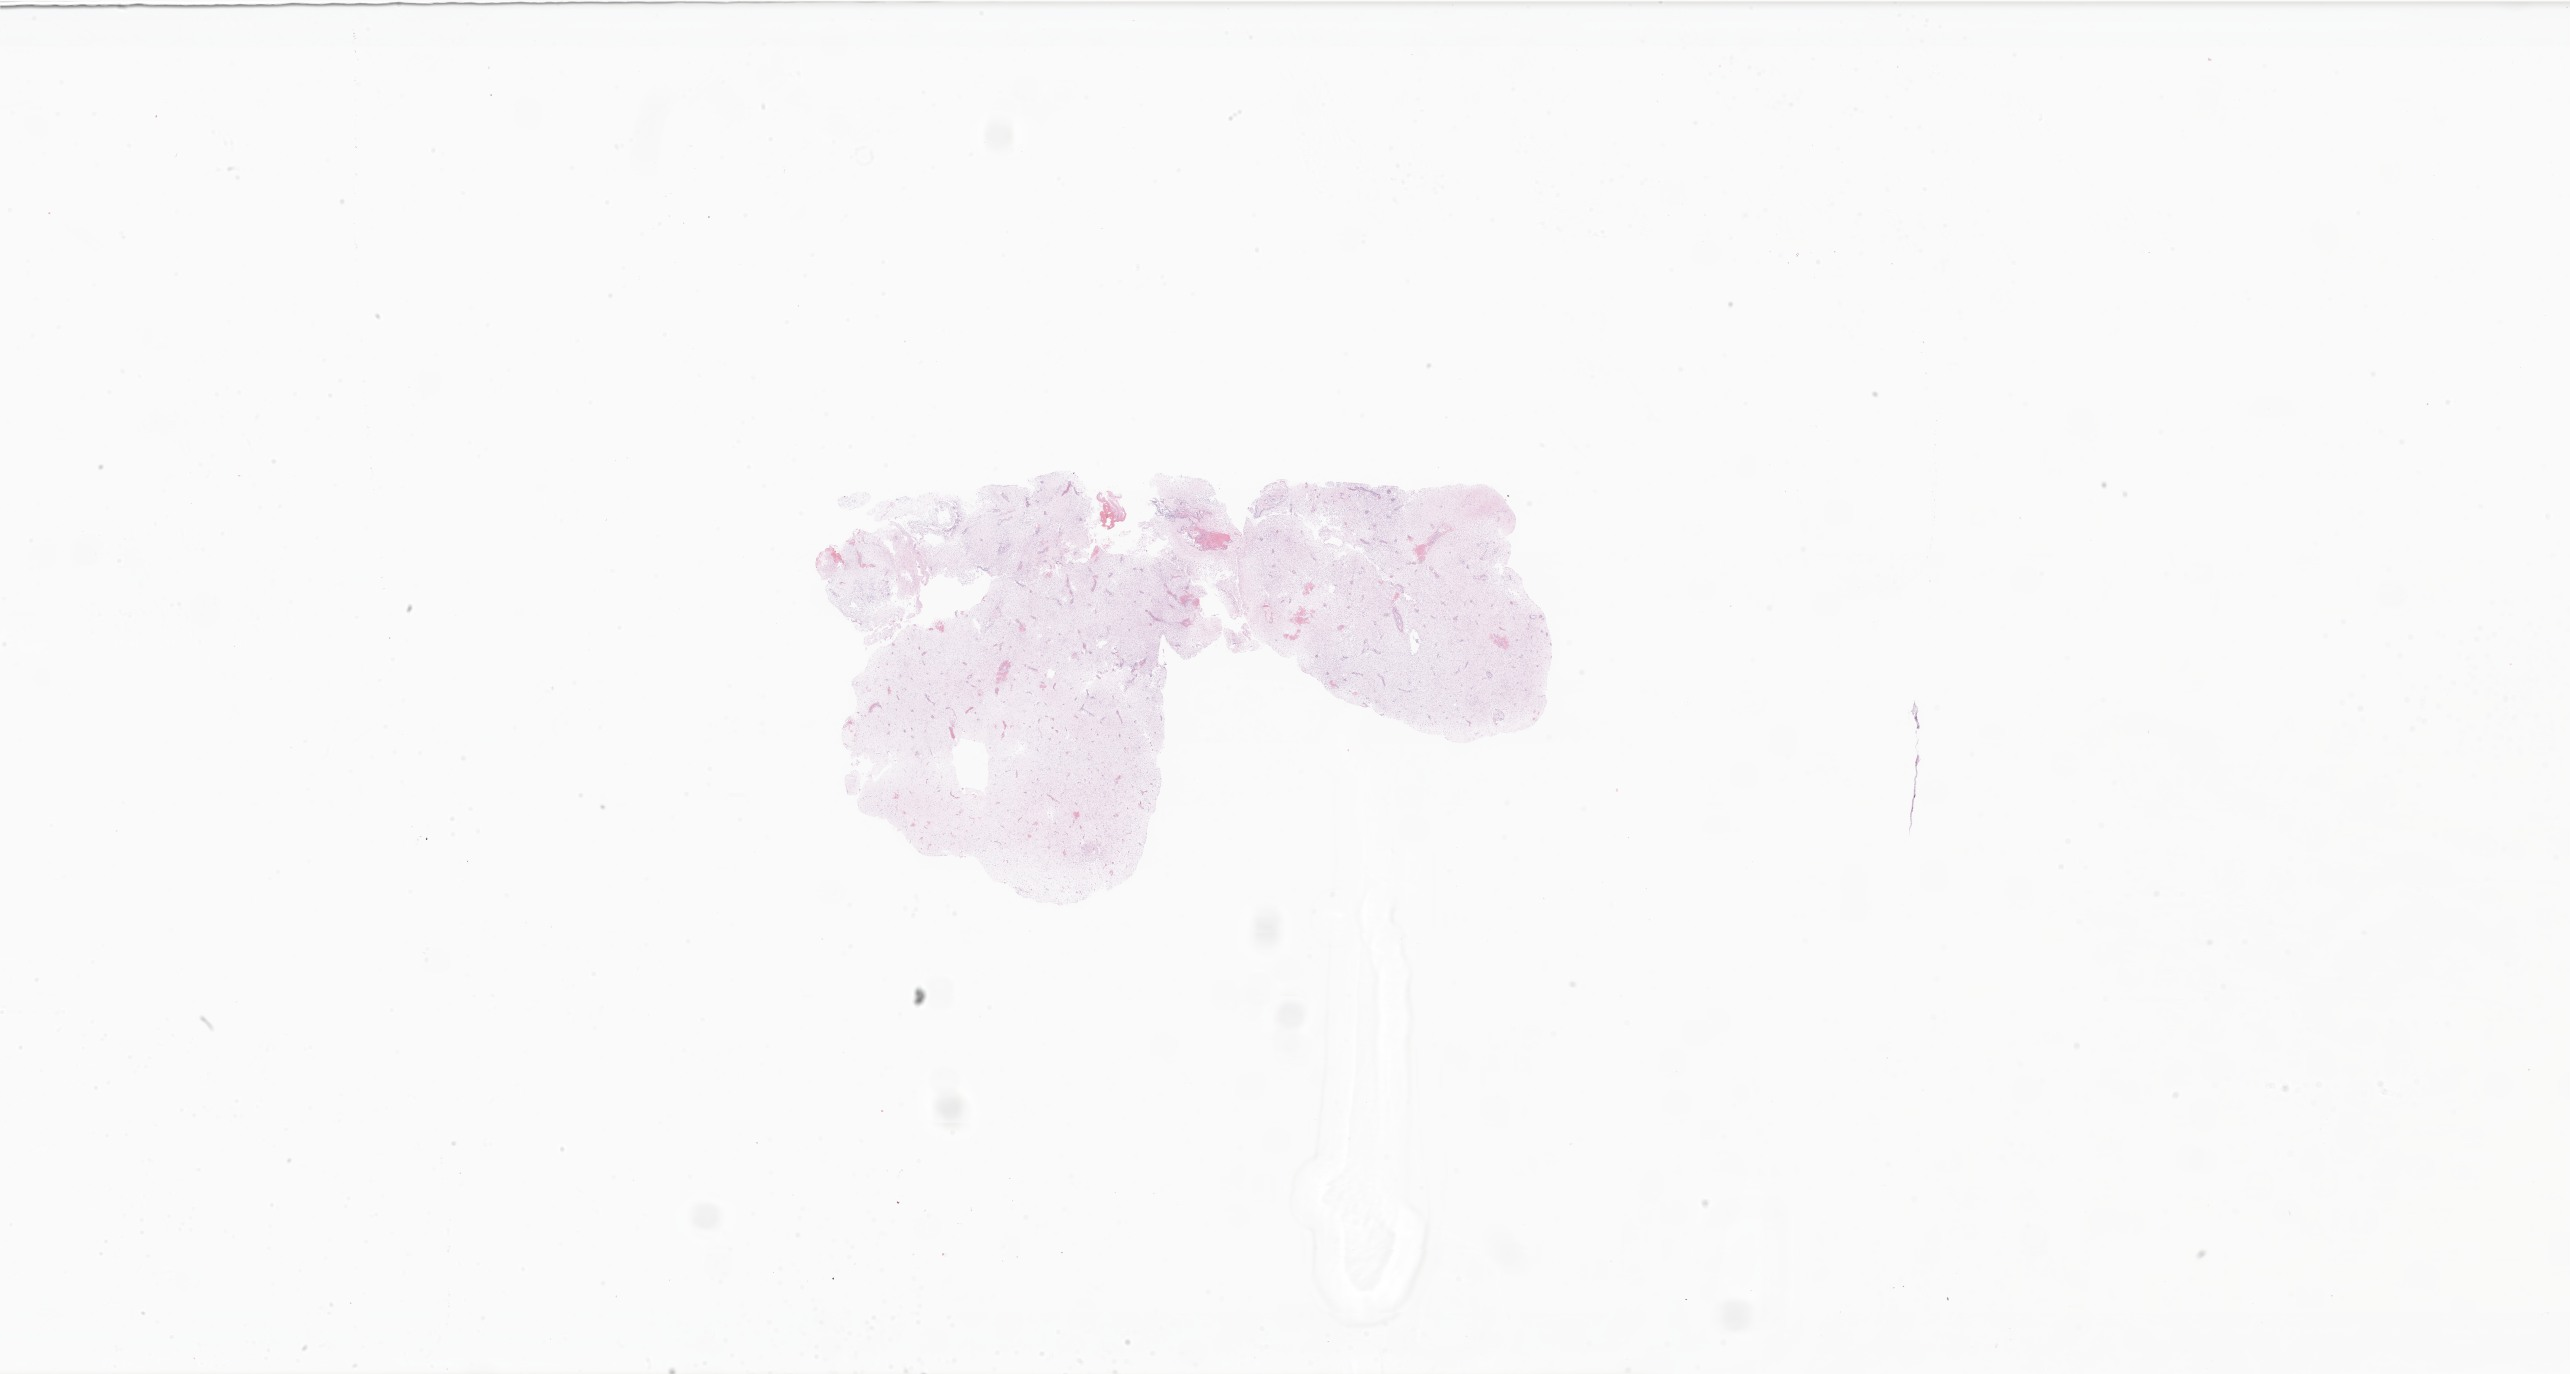
Whole-slide image, hematoxylin and eosin (H&E) stain of tumor tissue from the brain — whole scanned area (about 43.3 x 23.2 mm) shown as a low-resolution overview. FFPE section. Patient: male, age 43 months (3 years 7 months).
Diagnosis: Pilocytic astrocytoma.